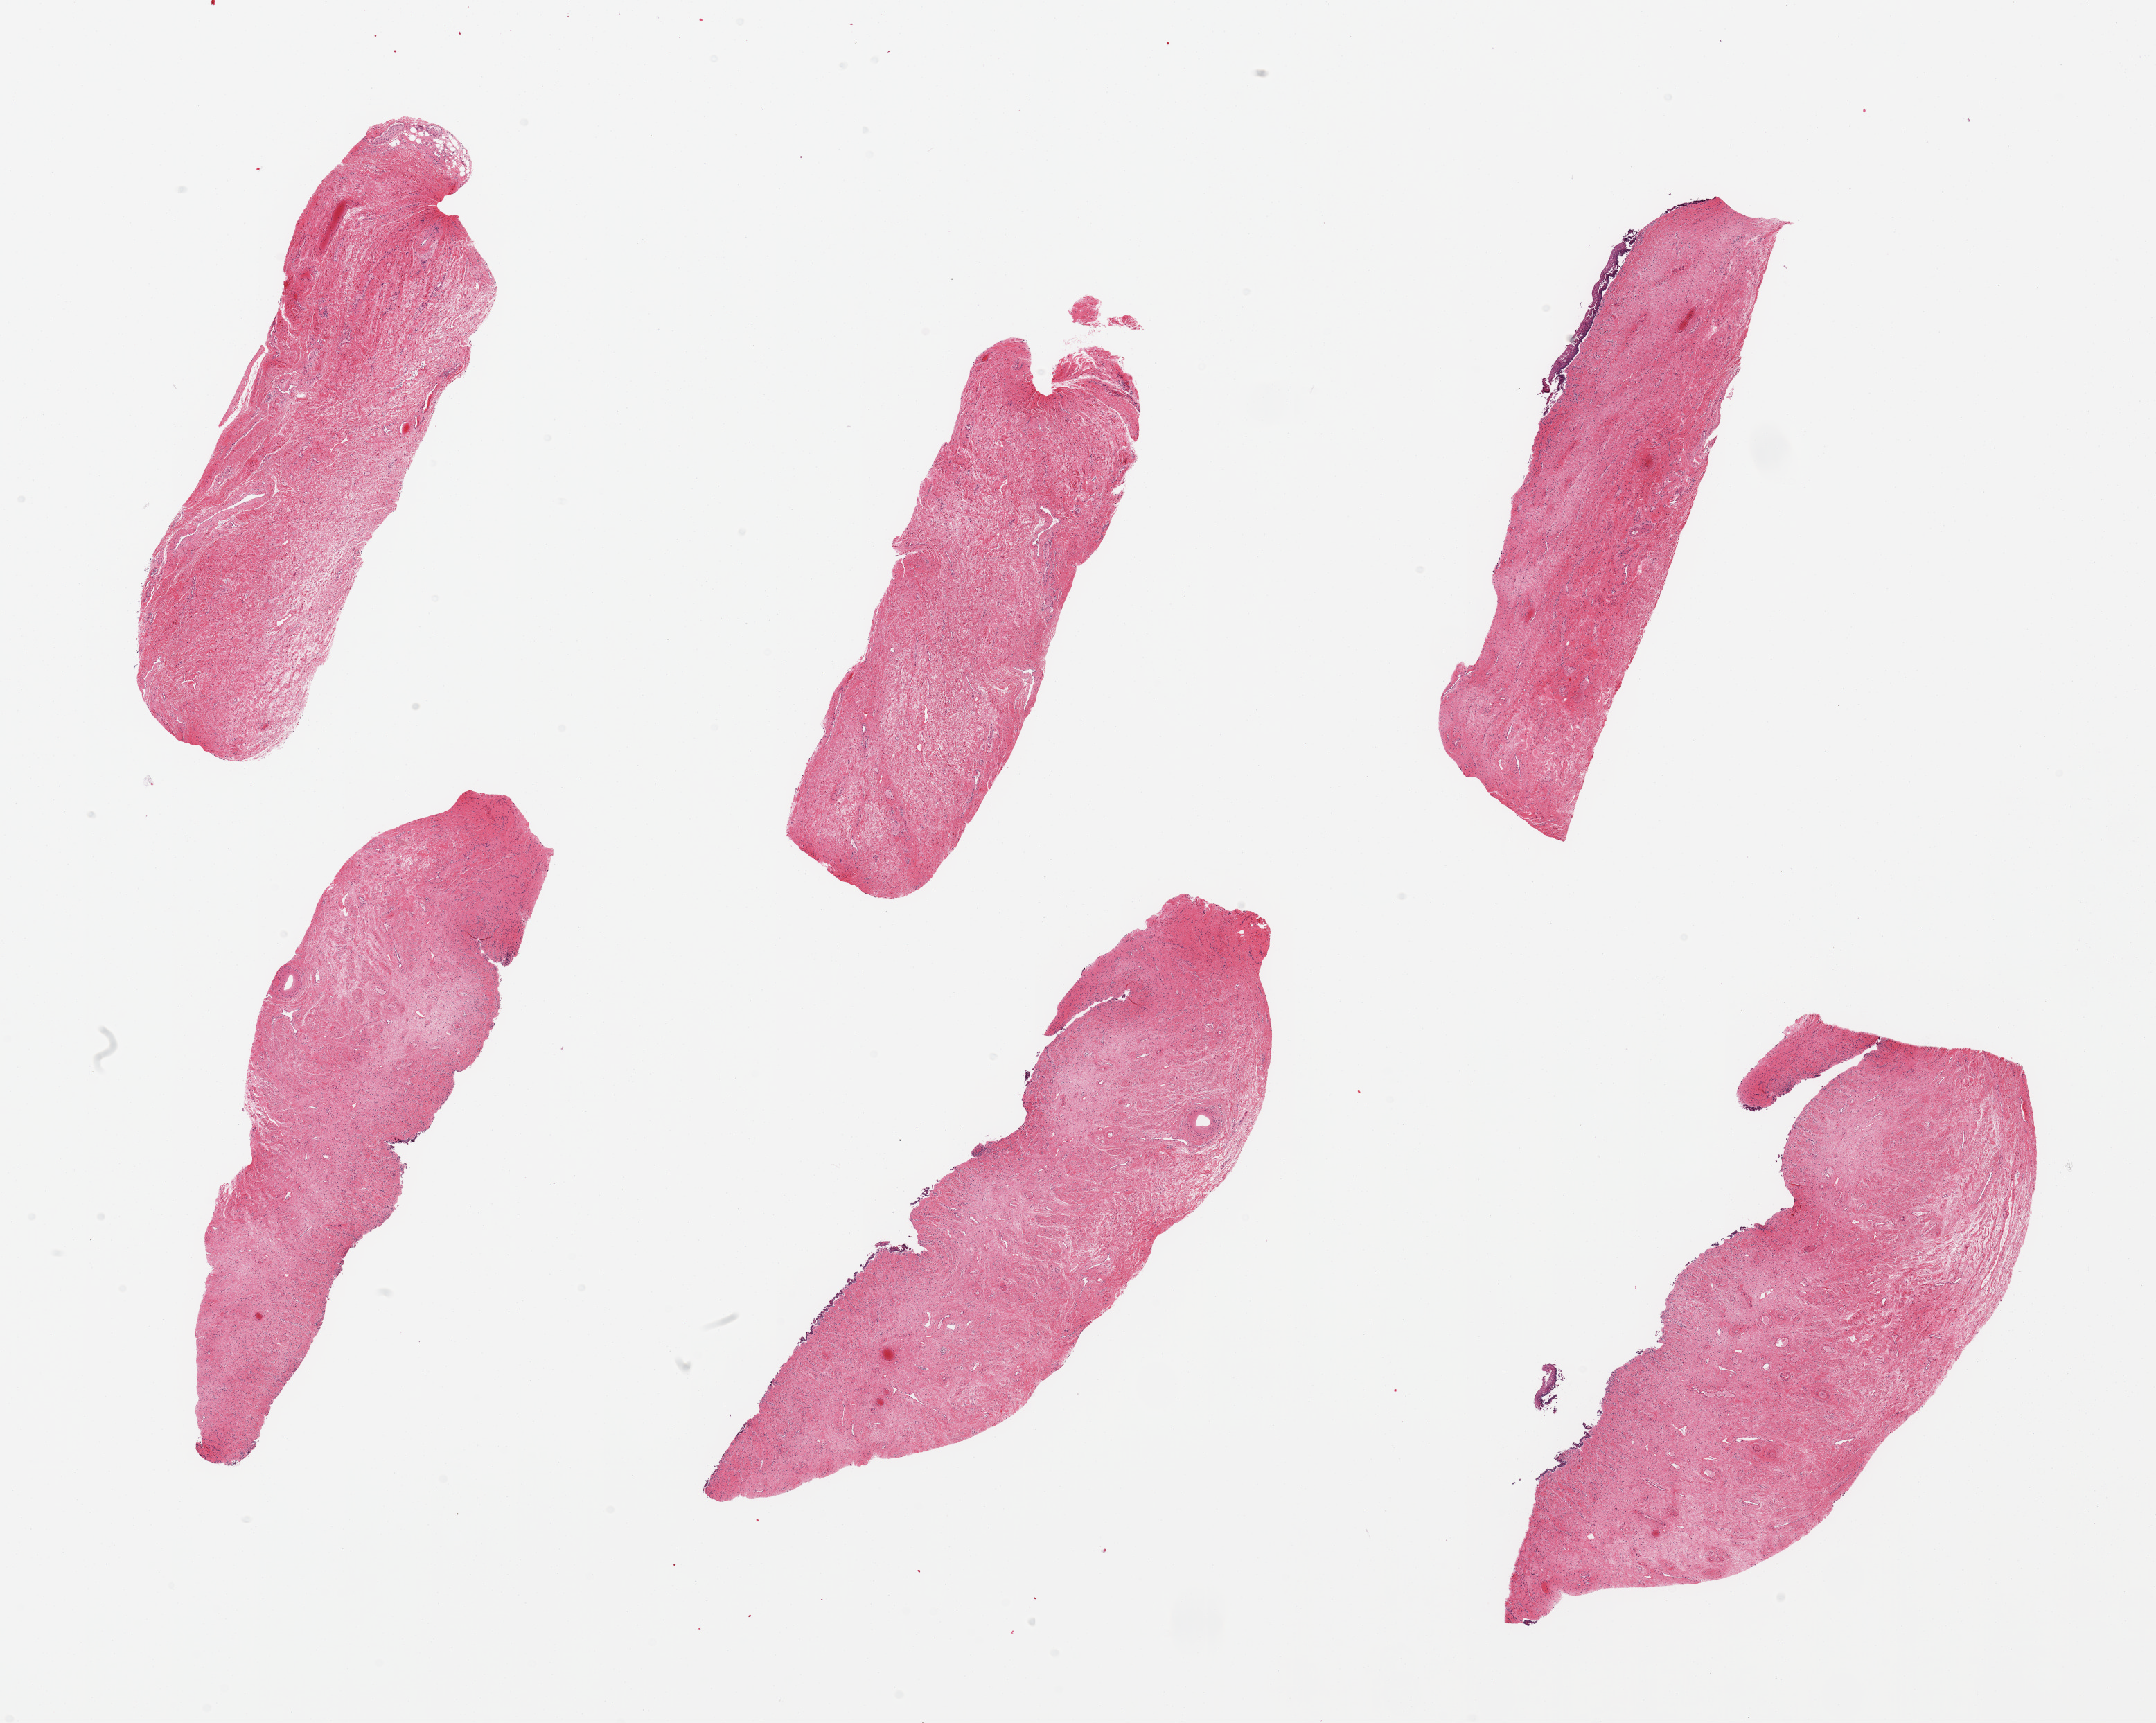
Whole-slide image, hematoxylin and eosin (H&E) stain, brightfield — shown as a low-resolution overview of the whole scanned area (about 24.6 x 19.7 mm). PAXgene-fixed paraffin-embedded (PFPE) section. Sampled site (target tissue): vagina. Donor tissue sample.
Review note (as recorded): 6 pieces; mucosa largely sloughed; wall intact.